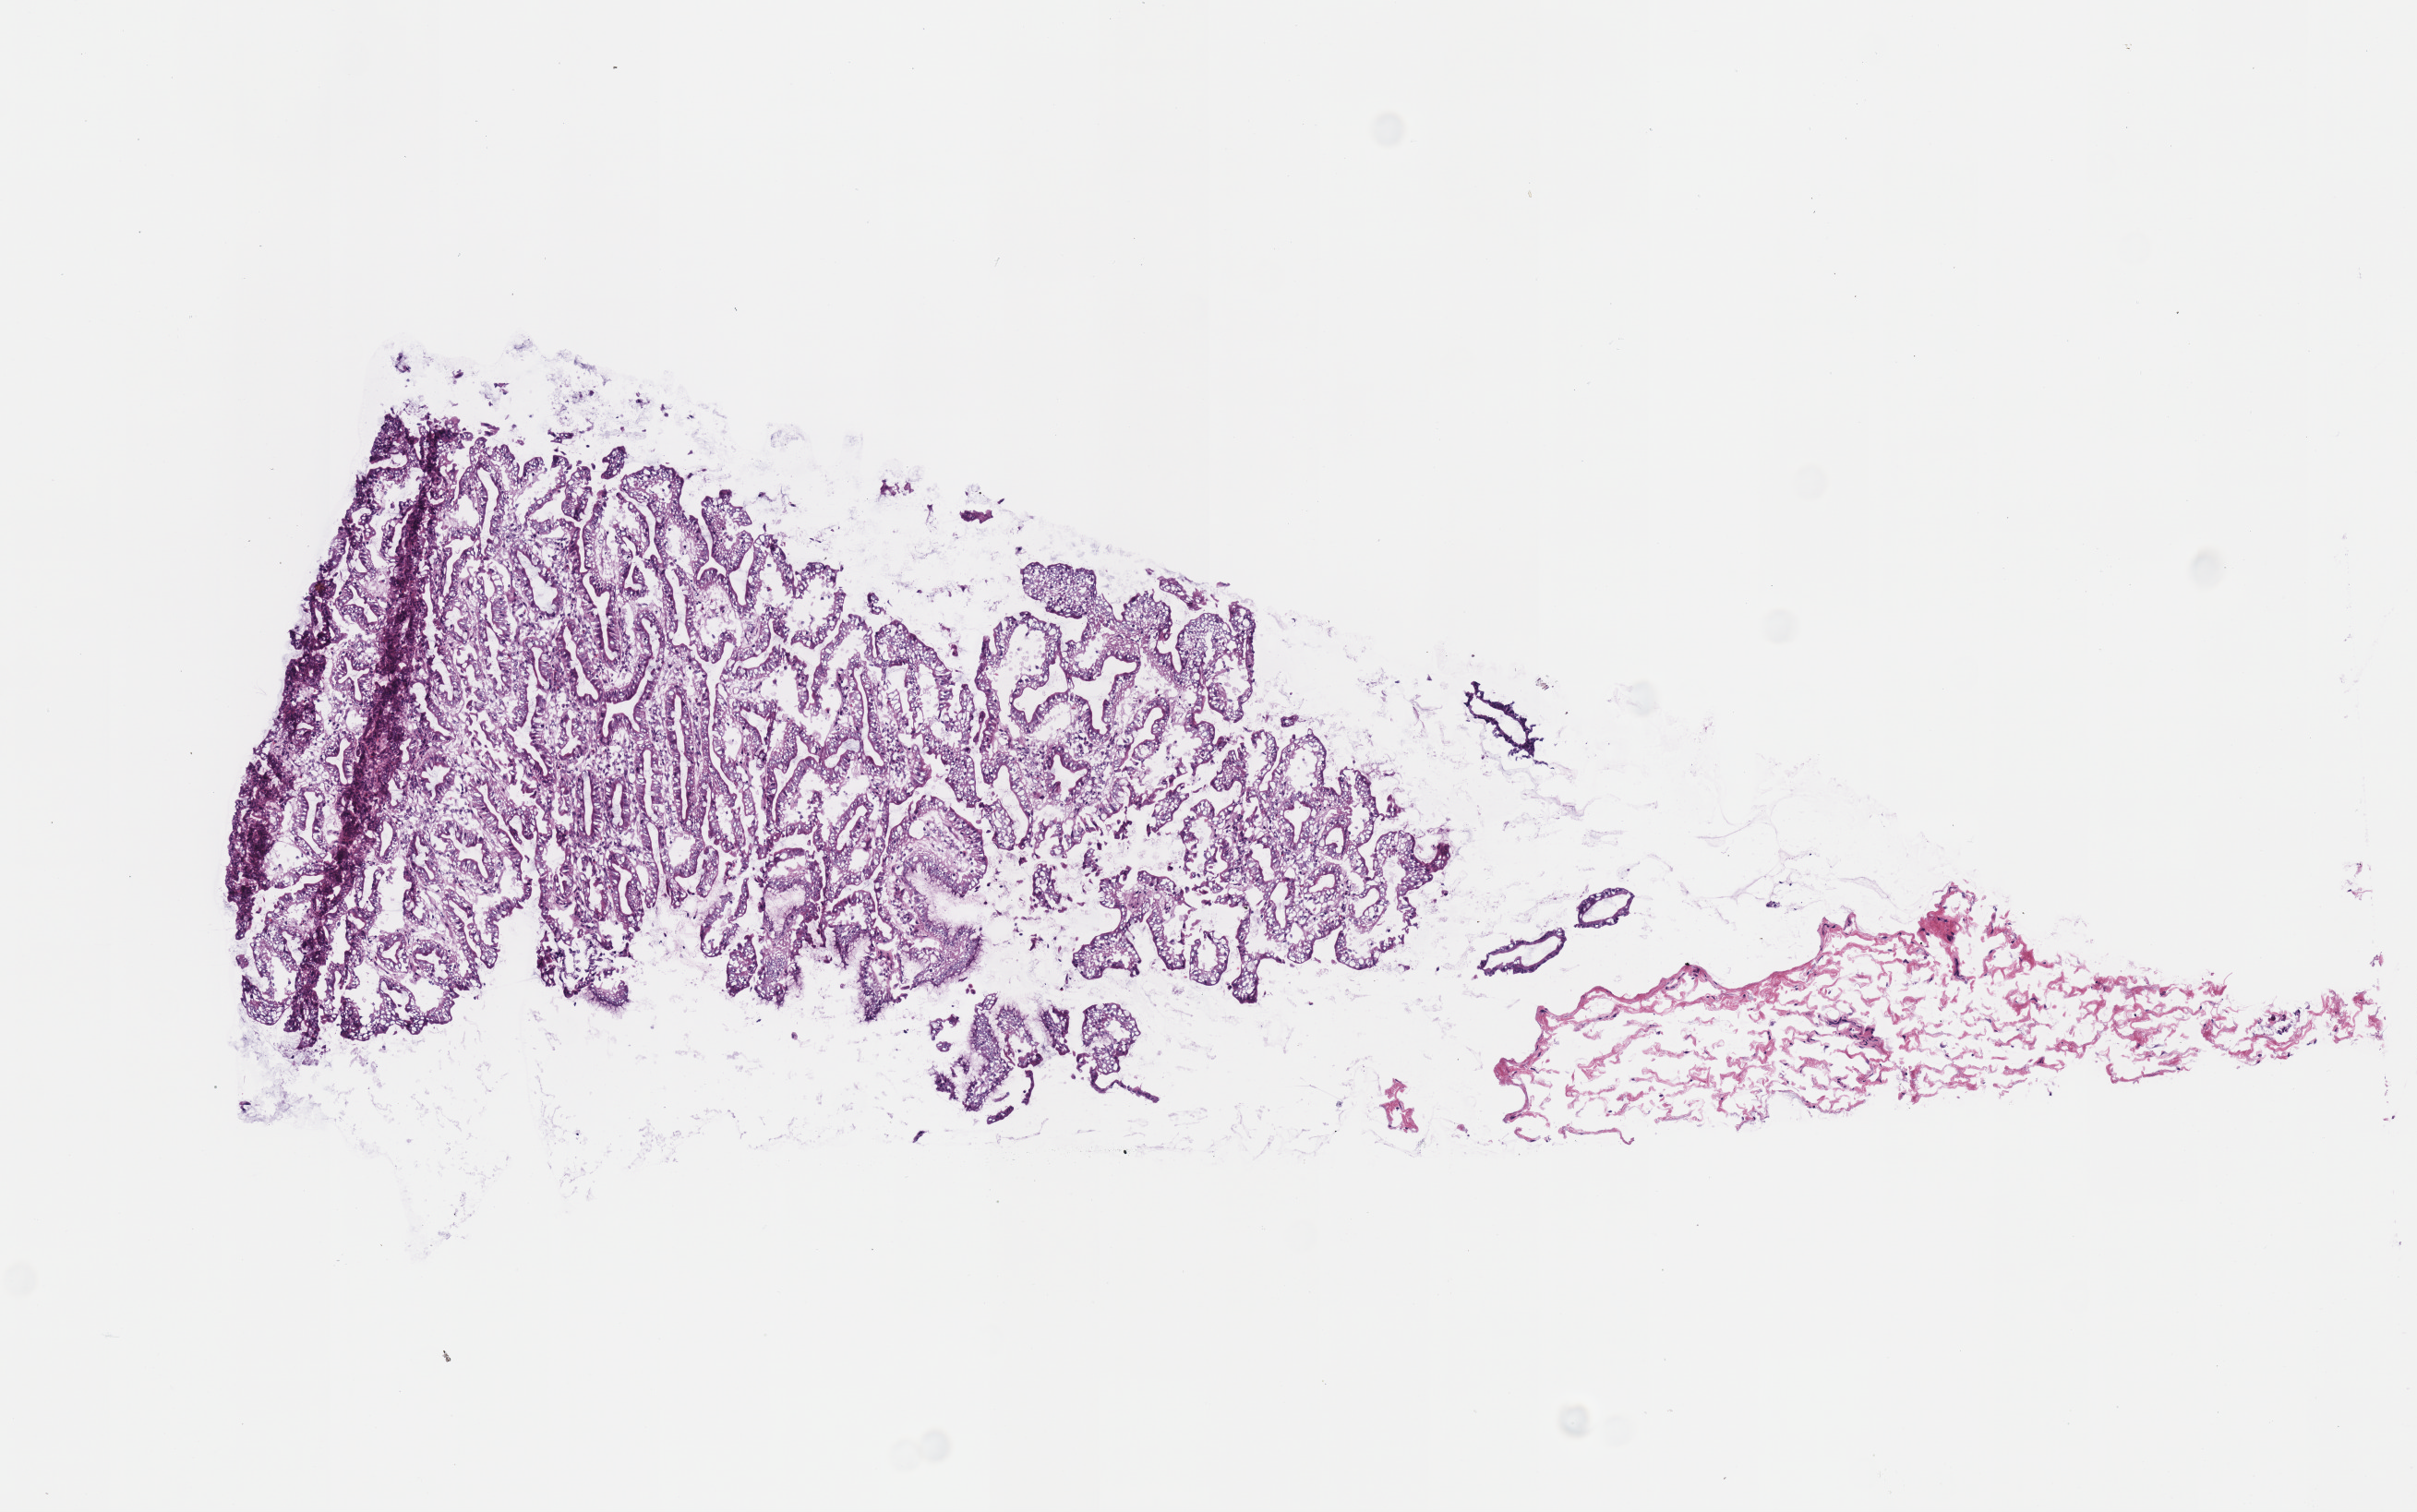
Hematoxylin and eosin (H&E) stained whole-slide image, low-resolution overview of the scanned area, about 5.2 x 3.2 mm; frozen section; solid tissue normal (non-tumour tissue) sample from the stomach. Male patient; age at initial diagnosis 72 years.
* this section: solid tissue normal sample (biorepository sample class)
* patient diagnosis: Papillary adenocarcinoma, NOS (body of stomach)